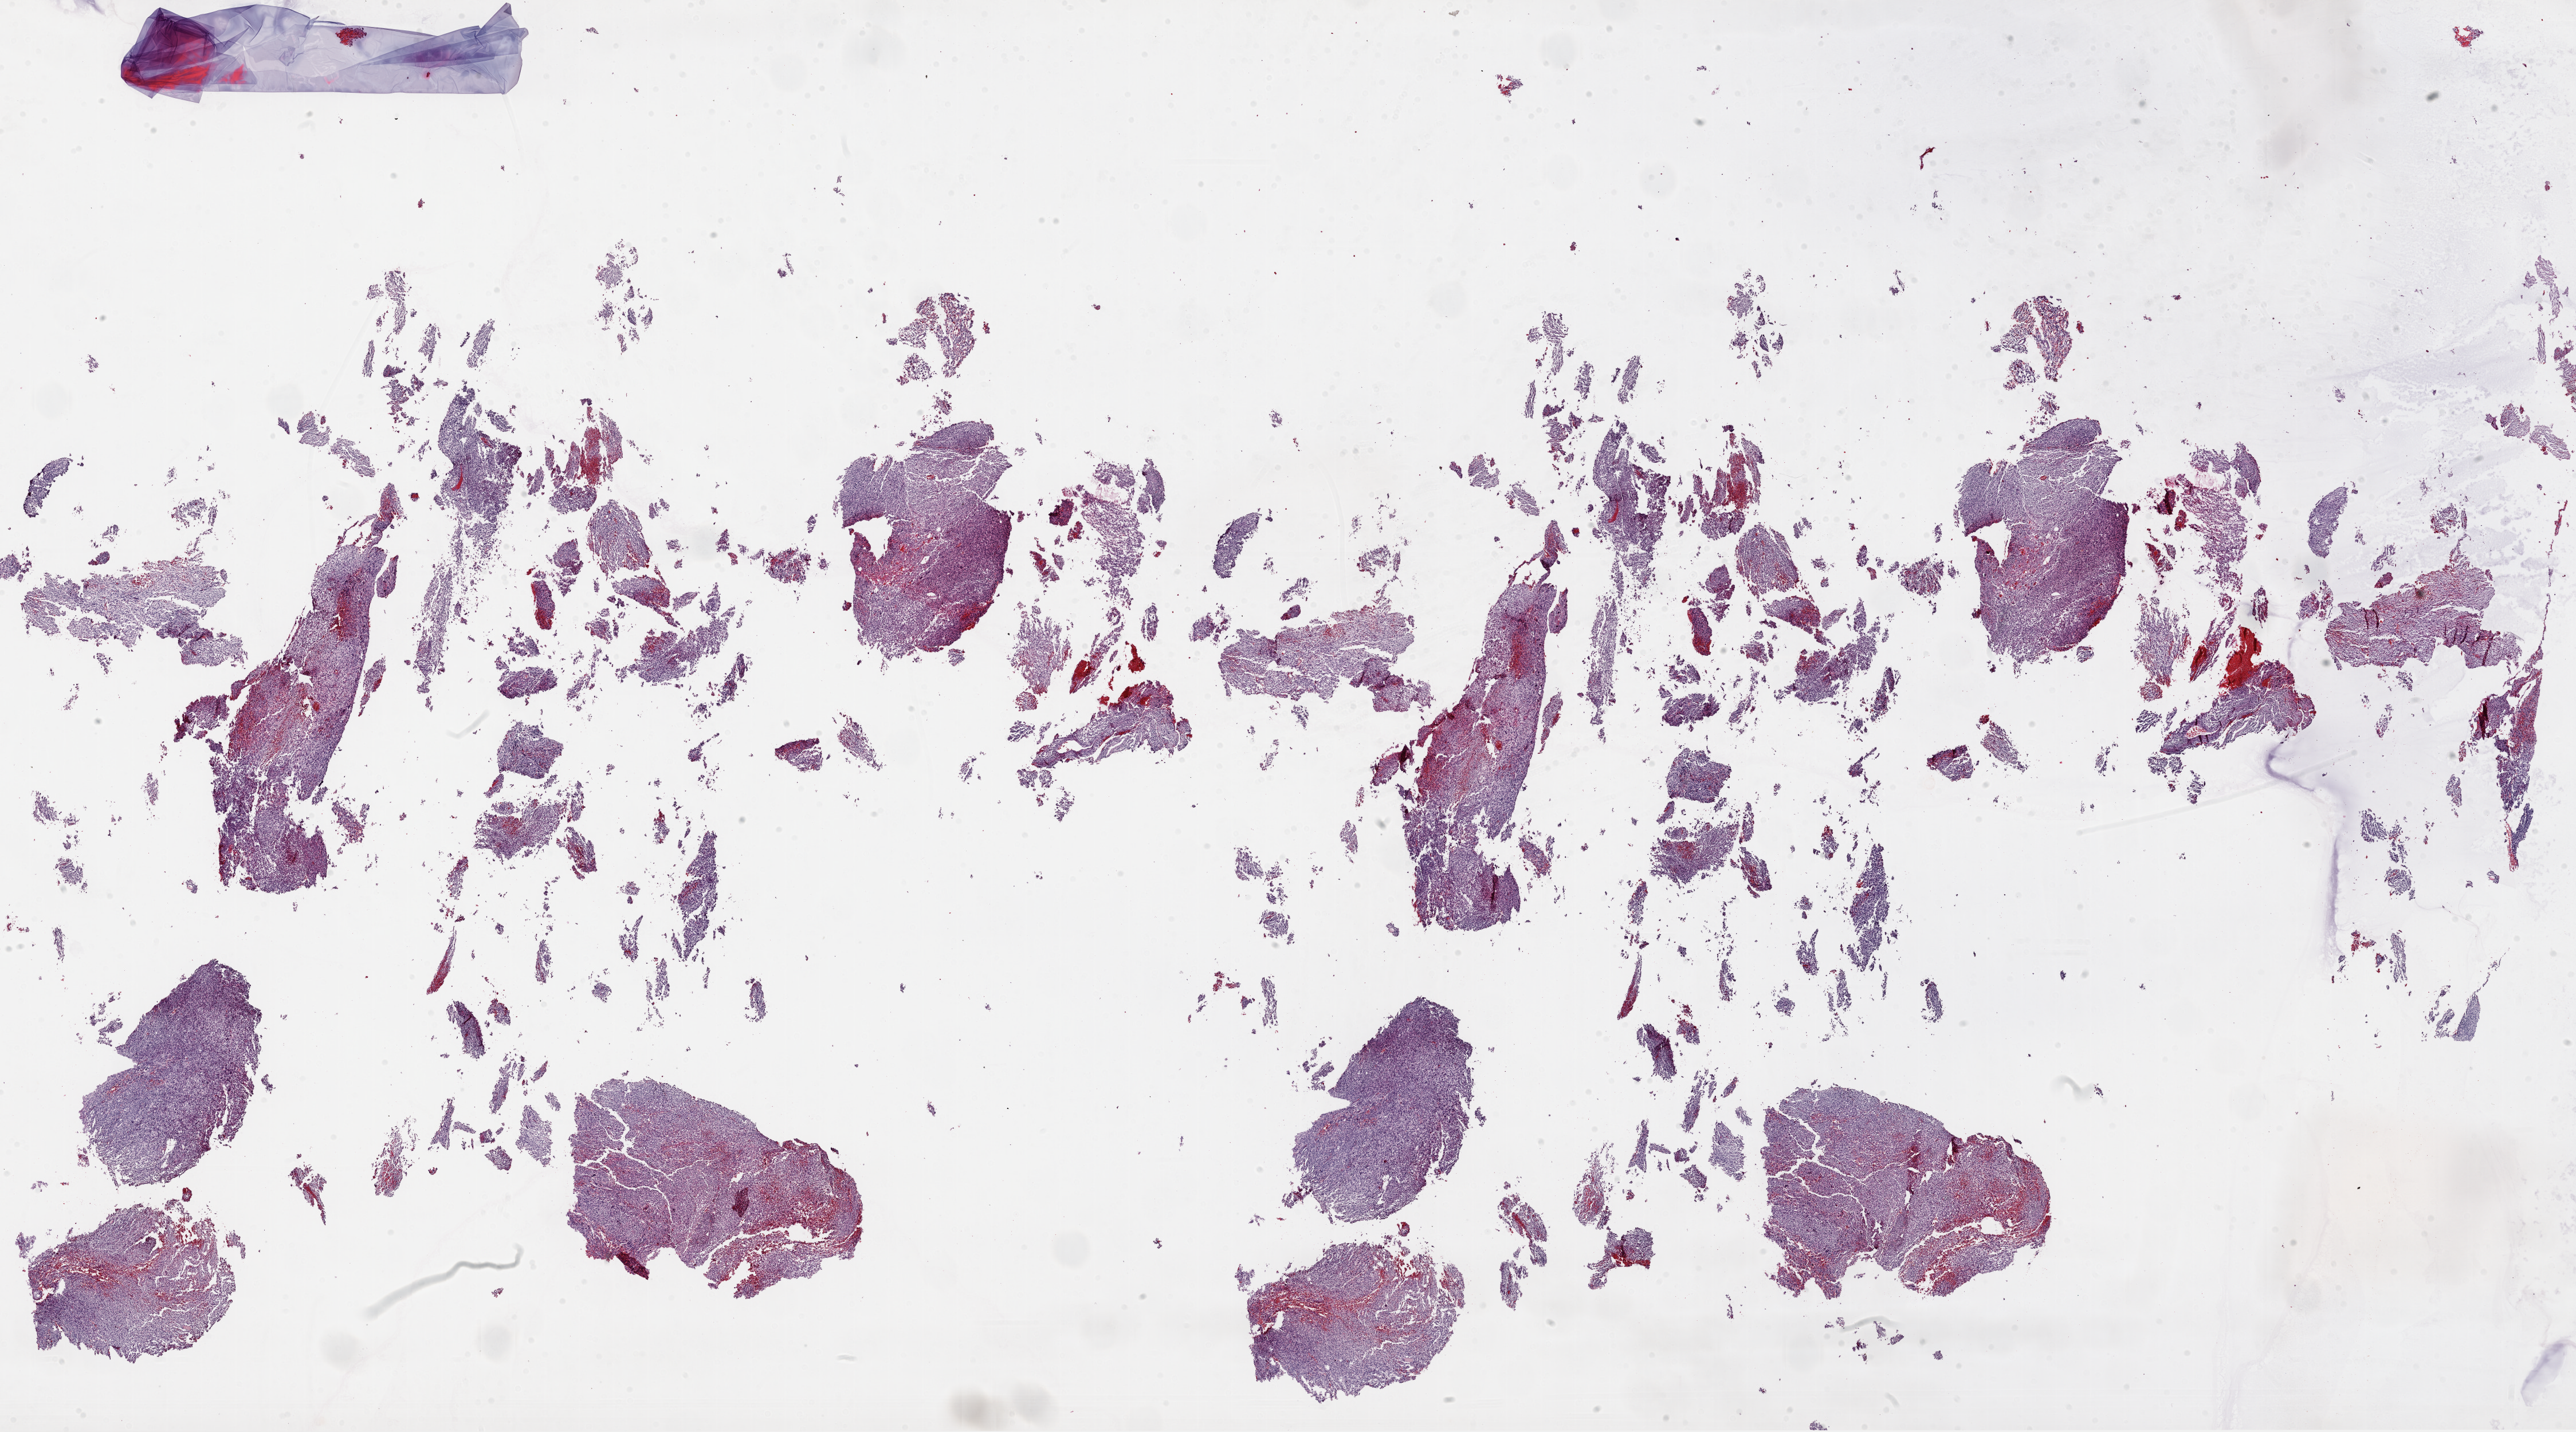
Digitized H&E-stained tissue section (whole slide), a low-resolution overview of the entire scanned area, about 36.3 x 20.2 mm, formalin-fixed paraffin-embedded (FFPE) diagnostic section, primary tumour sample from the brain. Female, age 74 years at initial diagnosis.
Histologic diagnosis: Glioblastoma.